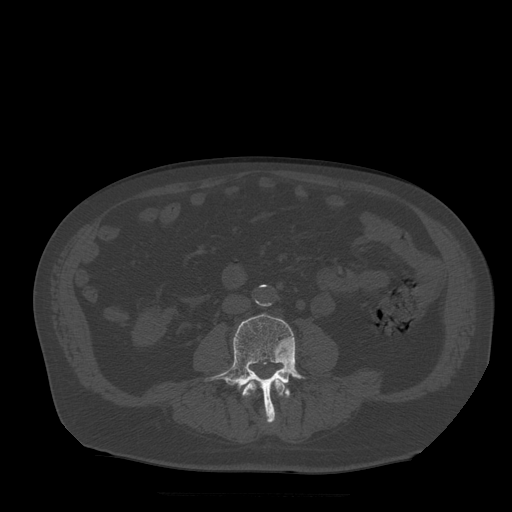
CT including the spine, one axial slice. Slice 118 of 522 in the series (ordered by position). Bone window (W 1800 / L 400 HU). 512 × 512 image matrix. Patient age 72 years. Case-level facts recorded for this patient, not image findings: primary cancer: prostate.
Outlined on this slice (semi-automatically segmented with operator editing):
- L3 vertebra: box from (x=243, y=378) to (x=291, y=398) px
- L4 vertebra: (x=204, y=314)–(x=307, y=423)